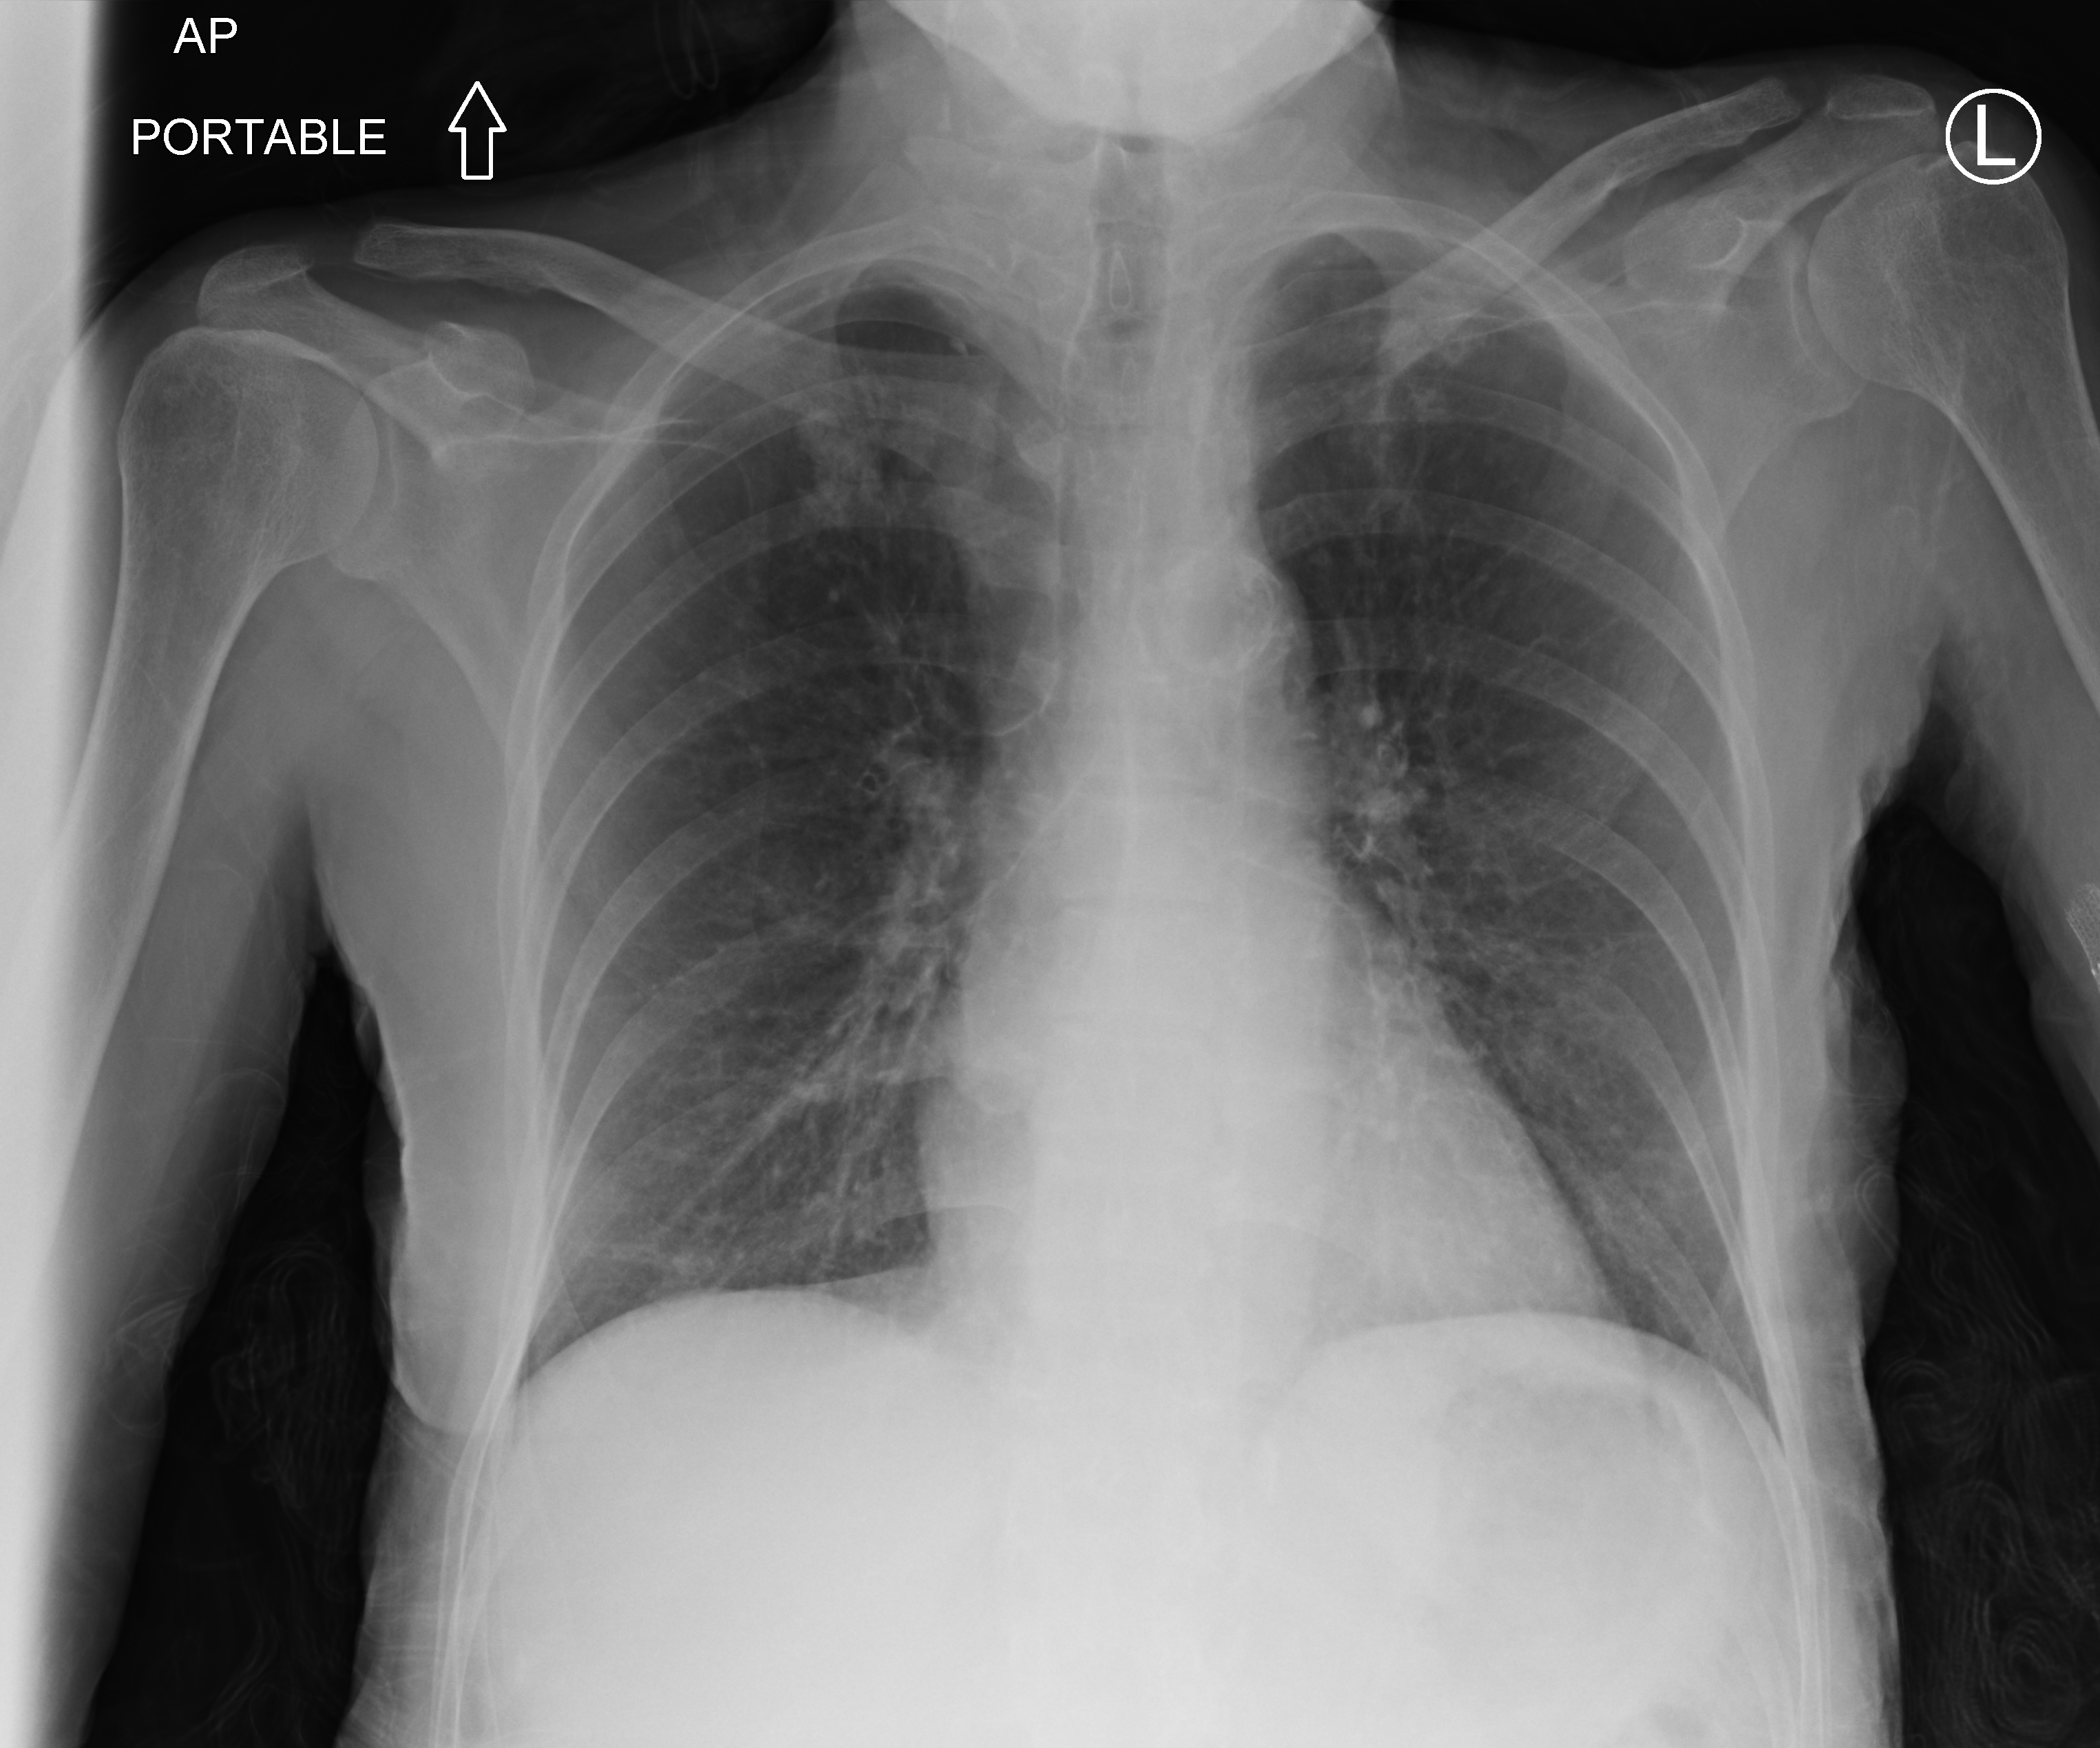
Chest X-ray (portable); anteroposterior (AP) projection. Female patient hospitalised with COVID-19, age 18–59 years.
Admission-level facts for this patient (not findings on this image; timing relative to this image not recorded): admitted to intensive care during this hospital stay: no.